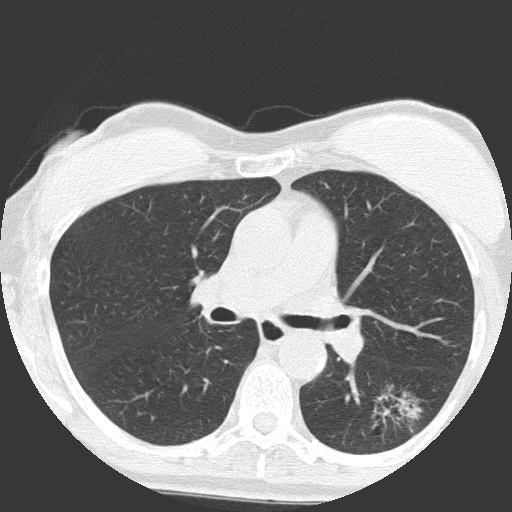
Chest CT (low-dose screening protocol), one axial image, baseline annual screen, lung window (W 1500 / L -600 HU), lung (sharp) reconstruction kernel (FC51), 512 × 512 image matrix. Female, age 64 years at enrolment. Former smoker at enrolment.
Lesion marked by an expert reader, box from (x=347, y=382) to (x=432, y=456) px. Screening reader's record for this exam (one nodule recorded; not confirmed to be the boxed lesion): non-calcified nodule or mass ≥4 mm, right upper lobe, 4 × 4 mm, poorly defined margins, ground glass attenuation. Note: the box lies in the patient's left hemithorax on this image, whereas the reader's record names the right lung; they may be different findings.